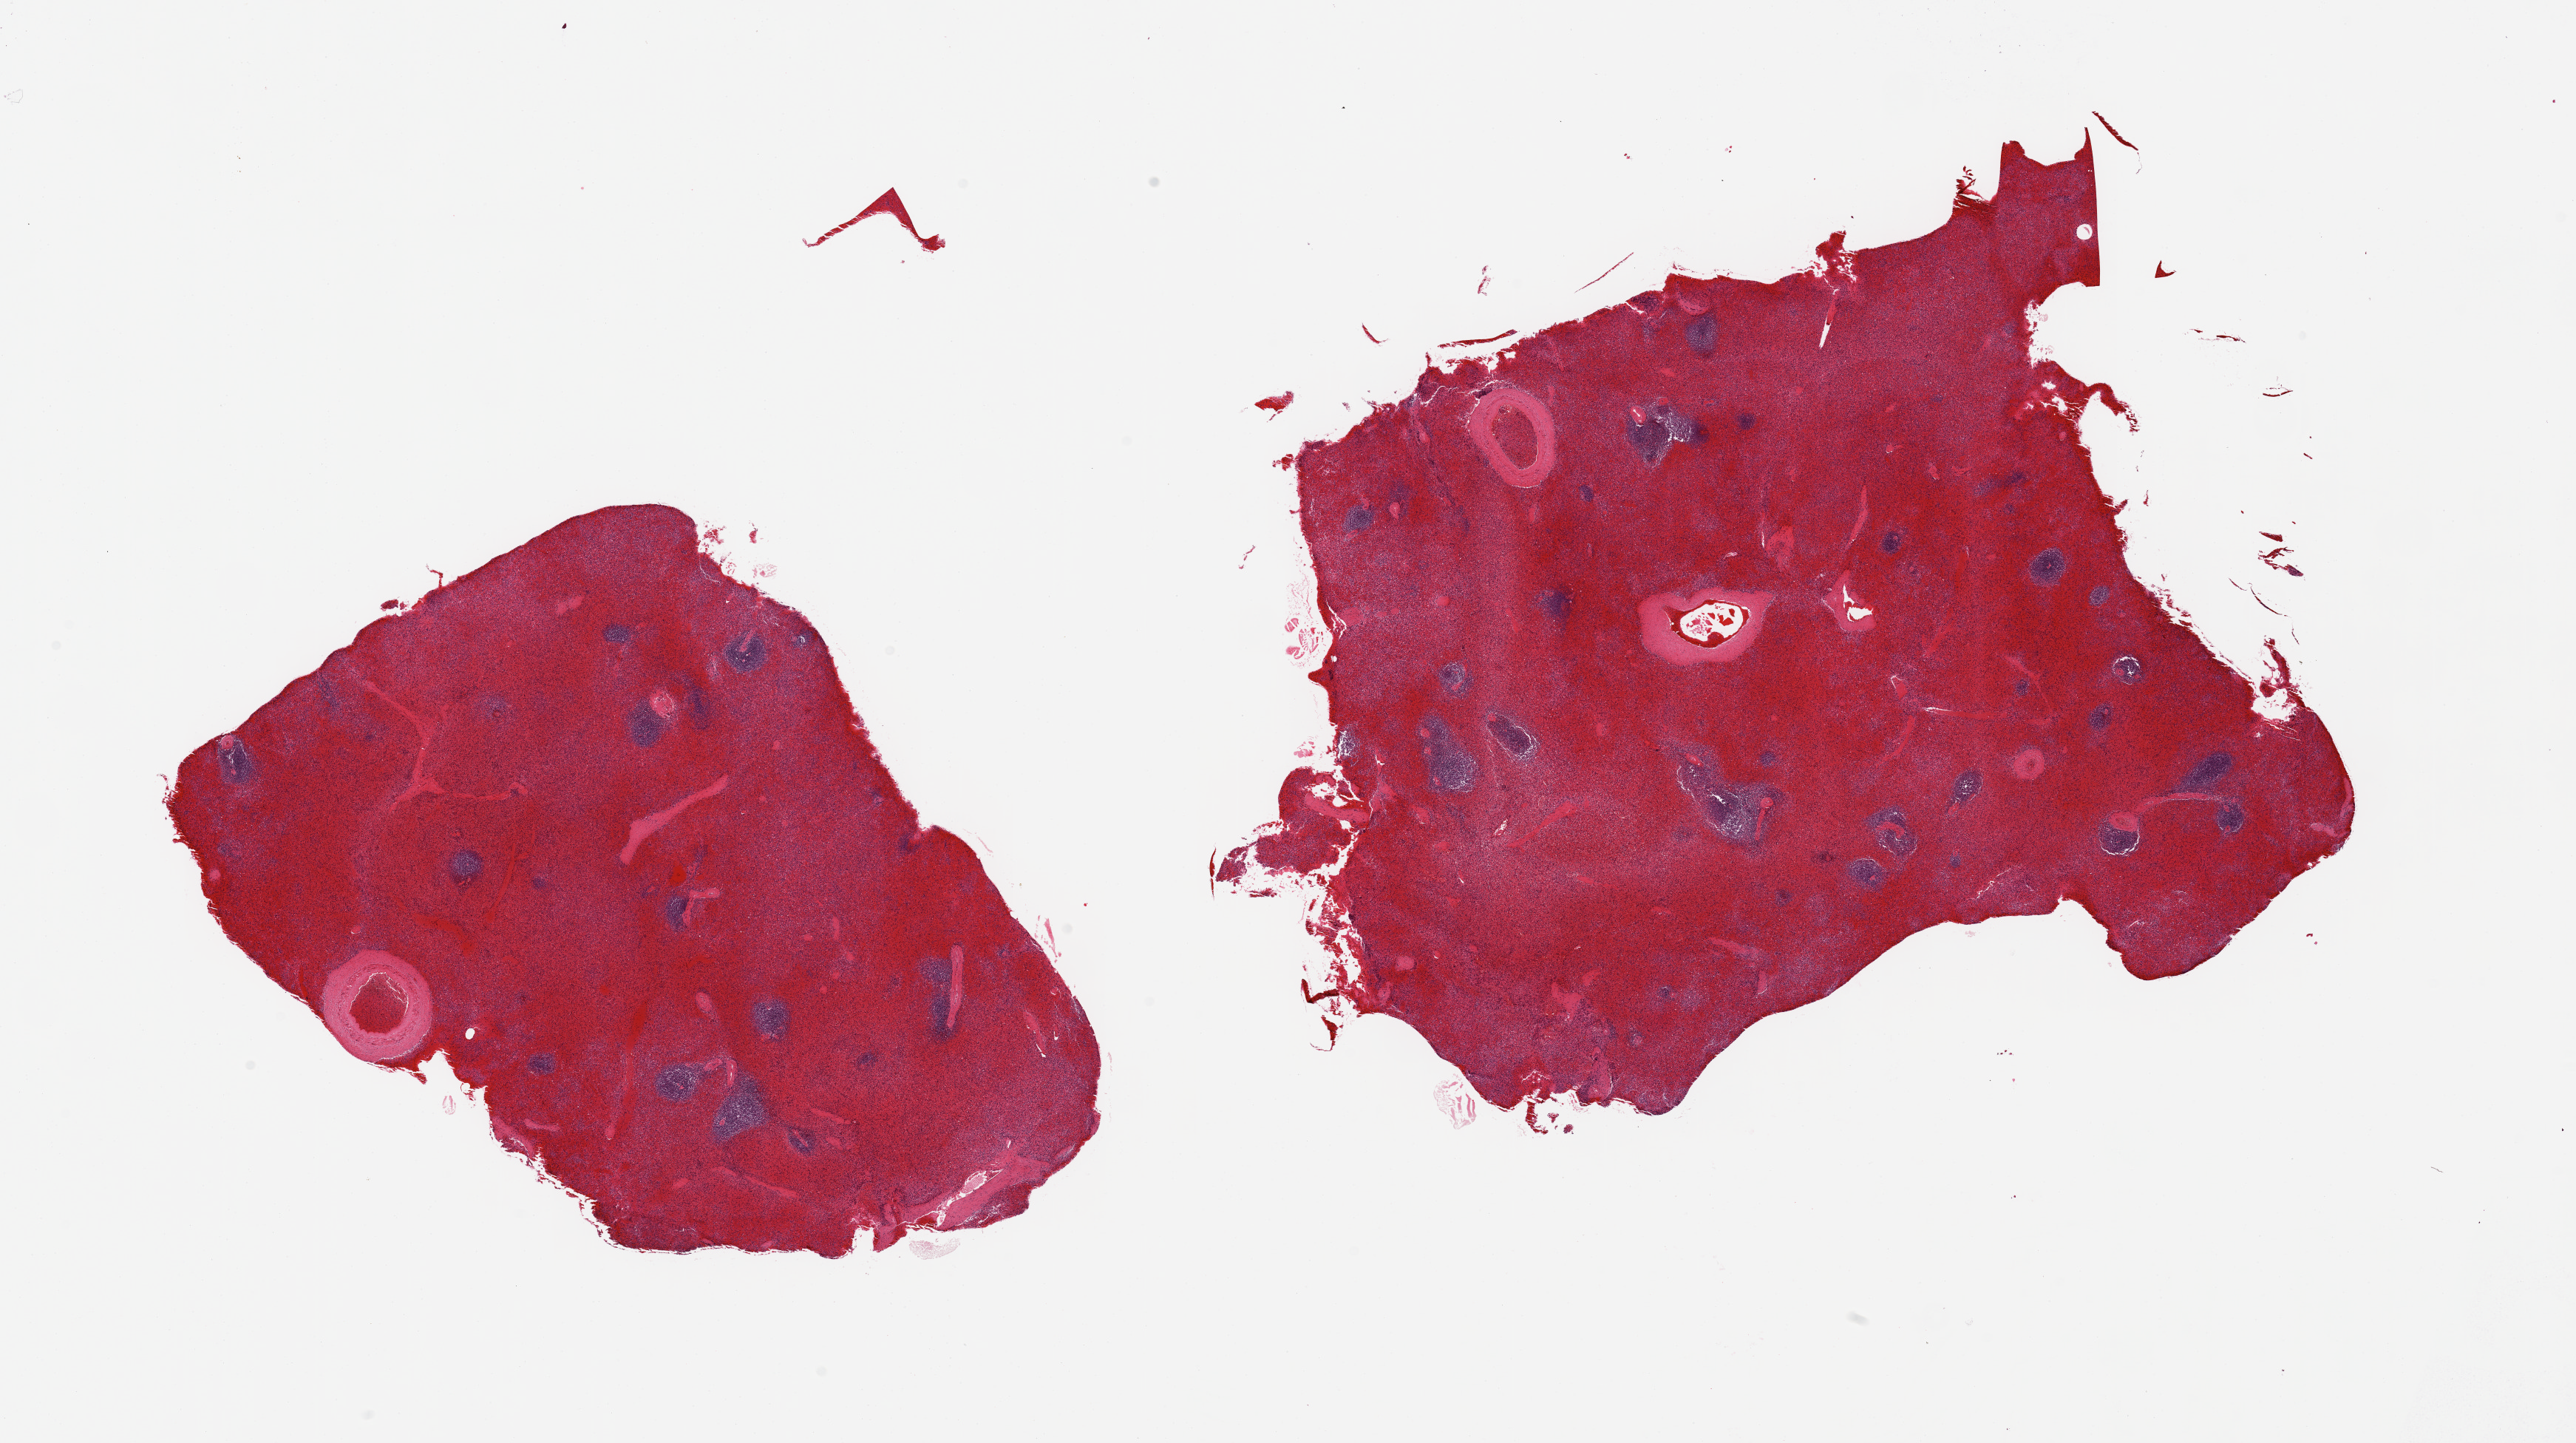
Whole-slide image, hematoxylin and eosin (H&E) stain, low-resolution overview of the scanned area, about 27.6 x 15.4 mm (slide scanned at 20x). PAXgene-fixed, paraffin-embedded tissue. Section of spleen (target tissue). Donor tissue sample. Male donor.
Review note (as recorded): 2 pieces; marked congestion.